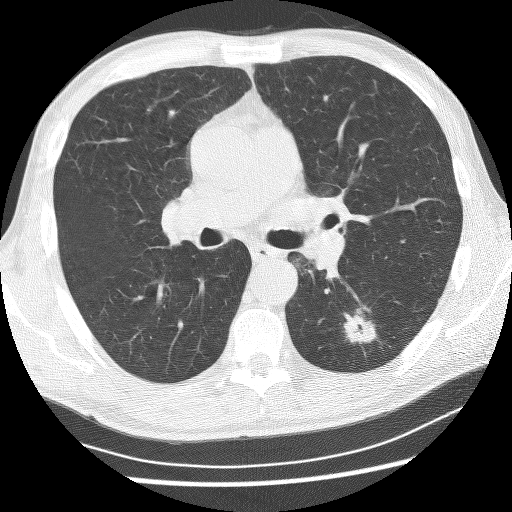
Low-dose screening chest CT, one axial slice; position 147 of 253 along the scan axis; lung window (W 1500 / L -600 HU); 2.5 mm slice thickness; 512 × 512 image matrix.
Outlined on this slice (outlined manually by an expert reader):
- lesion 1 (tumor, lower lobe of left lung): box from (x=344, y=310) to (x=376, y=344) px